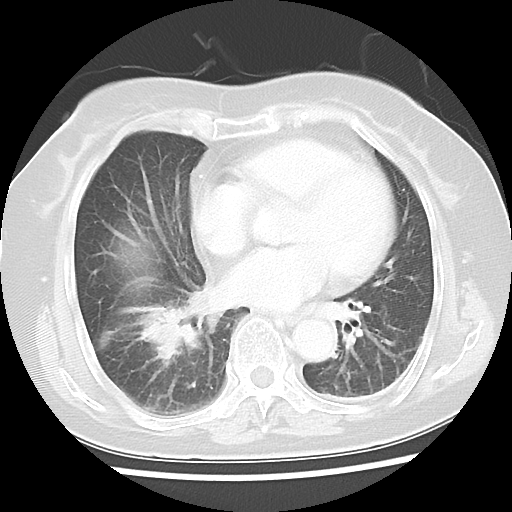
Chest CT, one axial slice. Slice 18 of 45 in the series (ordered by position). Reconstruction kernel LUNG. Lung window (W 1500 / L -600 HU). 512 × 512 image matrix, field of view 312 × 312 mm. Female patient, age 65 years. Case-level facts recorded for this patient, not image findings: clinical TNM (as recorded): T2 N3 M0.
Annotated regions visible in this slice (bounding box drawn by a radiologist):
- lung tumour (recorded histology: adenocarcinoma): box from (x=142, y=301) to (x=204, y=365) px